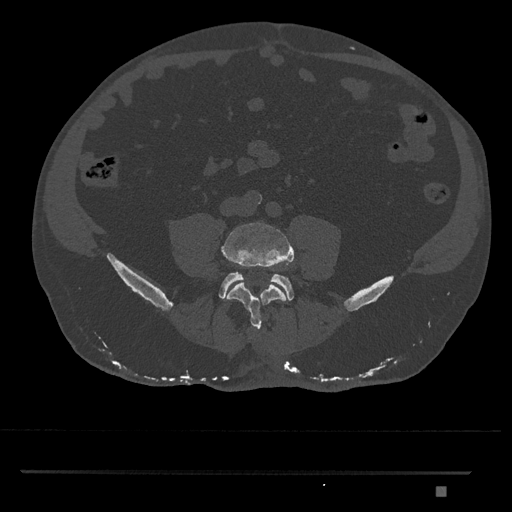
CT including the spine, one axial slice. Position 590 of 1134 along the scan axis. Reconstruction kernel Br40s/3. 120 kVp. Bone window (W 1800 / L 400 HU). 0.5 mm slice thickness. 512 × 512 image matrix. Male patient, age 65 years. From the clinical record (not read from this slice): primary cancer: prostate.
Annotated regions visible in this slice (semi-automatically segmented with operator editing):
- L4 vertebra: box from (x=221, y=222) to (x=294, y=330) px
- L5 vertebra: (x=219, y=272)–(x=294, y=300)